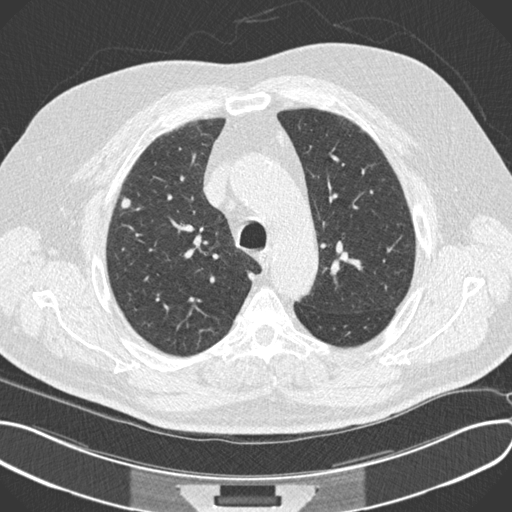
Chest CT (low-dose screening protocol), one axial image, third screening round (two years after baseline), lung window (W 1500 / L -600 HU), slice 54 of 212 in the series. Male participant, aged 64 years at enrolment. Current smoker at enrolment.
Lesion marked by an expert reader, box from (x=108, y=187) to (x=141, y=223) px. Reader record for this screening exam (exam-level; its link to the box is not recorded): non-calcified nodule or mass ≥4 mm, right upper lobe, 7 × 6 mm, smooth margins, soft tissue attenuation, pre-existing on the prior screen: no. Official screen result: positive, other. Later outcome: lung cancer diagnosed 104 days after this screen — squamous cell carcinoma, NOS, right upper lobe, moderately differentiated (G2), stage IA (AJCC 6th edition), 7 mm at pathology.